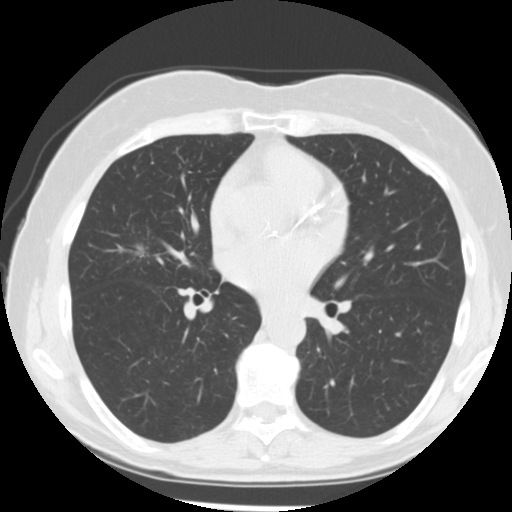
Low-dose screening chest CT, one axial slice; position 140 of 255 along the scan axis; reconstruction kernel STANDARD; 120 kVp; lung window (W 1500 / L -600 HU); 512 × 512 image matrix, field of view 320 × 320 mm.
Structures marked on this image (outlined manually by an expert reader):
- lesion 1 (tumor, middle lobe of right lung): bounding box [x1, y1, x2, y2] px = [137, 247, 144, 257]